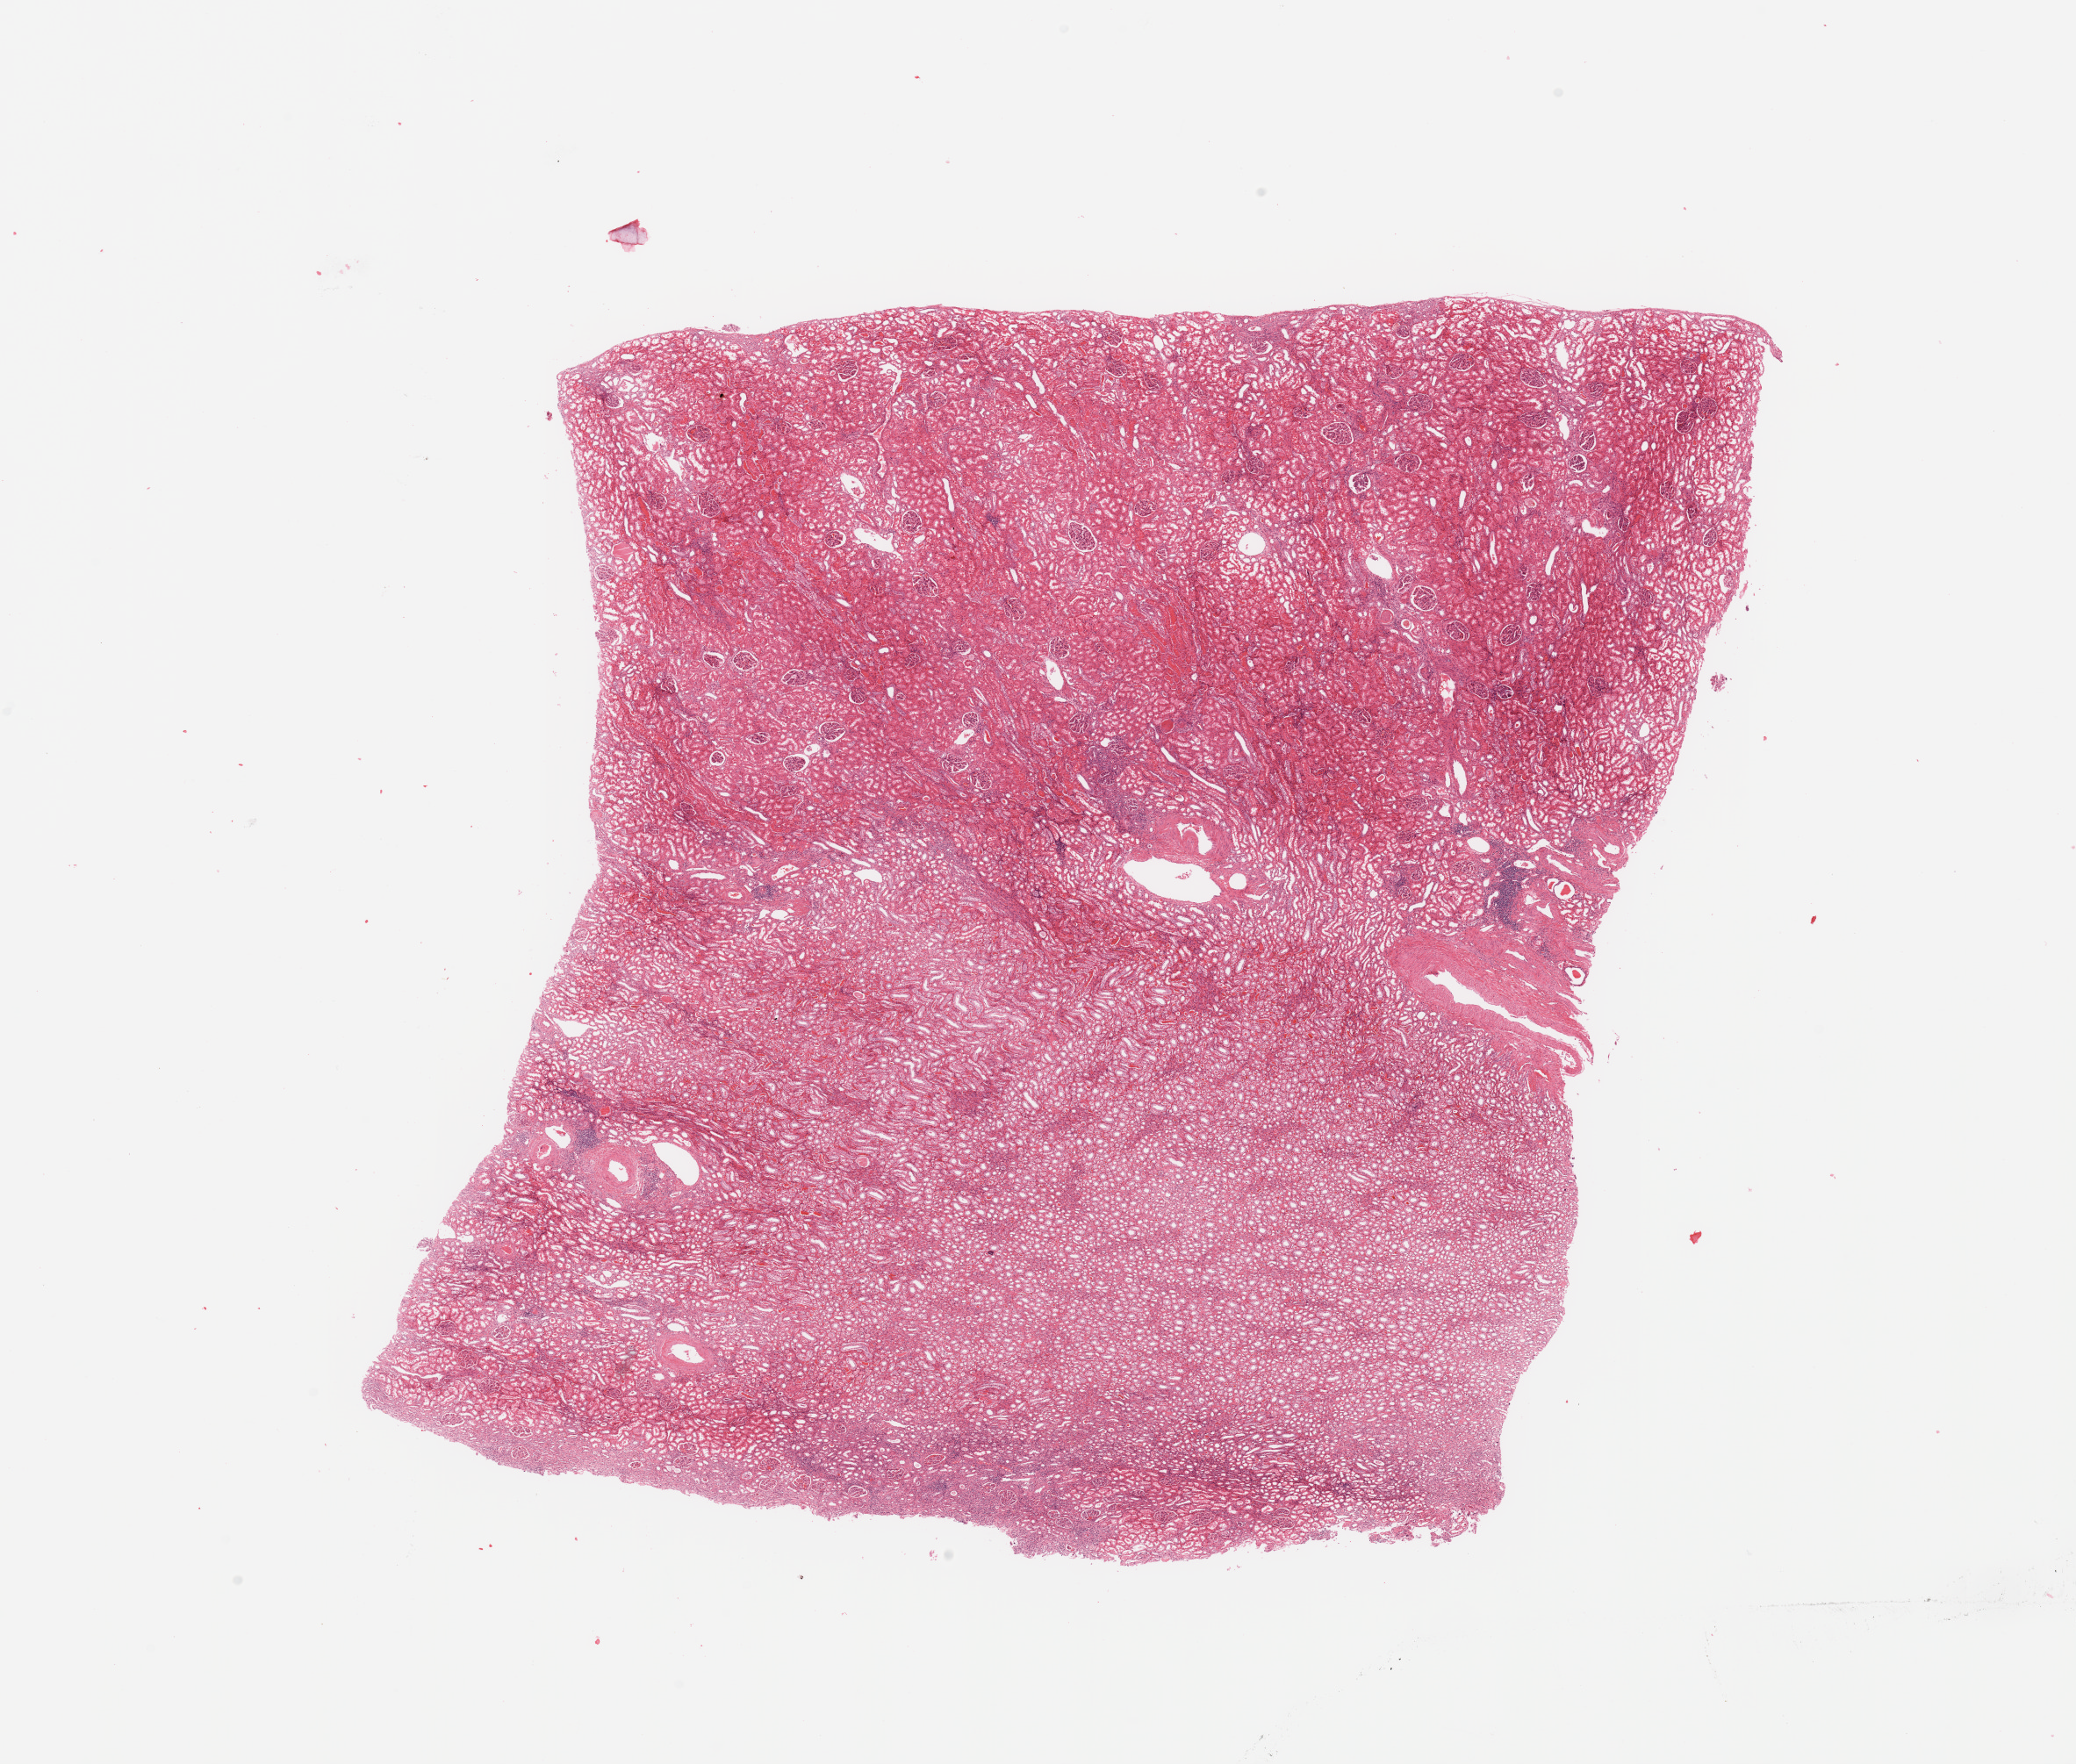
Digitized H&E tissue section (whole slide), whole scanned area (about 18.7 x 15.9 mm) shown as a low-resolution overview. Normal (non-tumour) tissue sample, kidney. Female, 55 y/o.
This section: normal (non-tumour) tissue from the same patient. Patient diagnosis: Renal cell carcinoma, NOS.